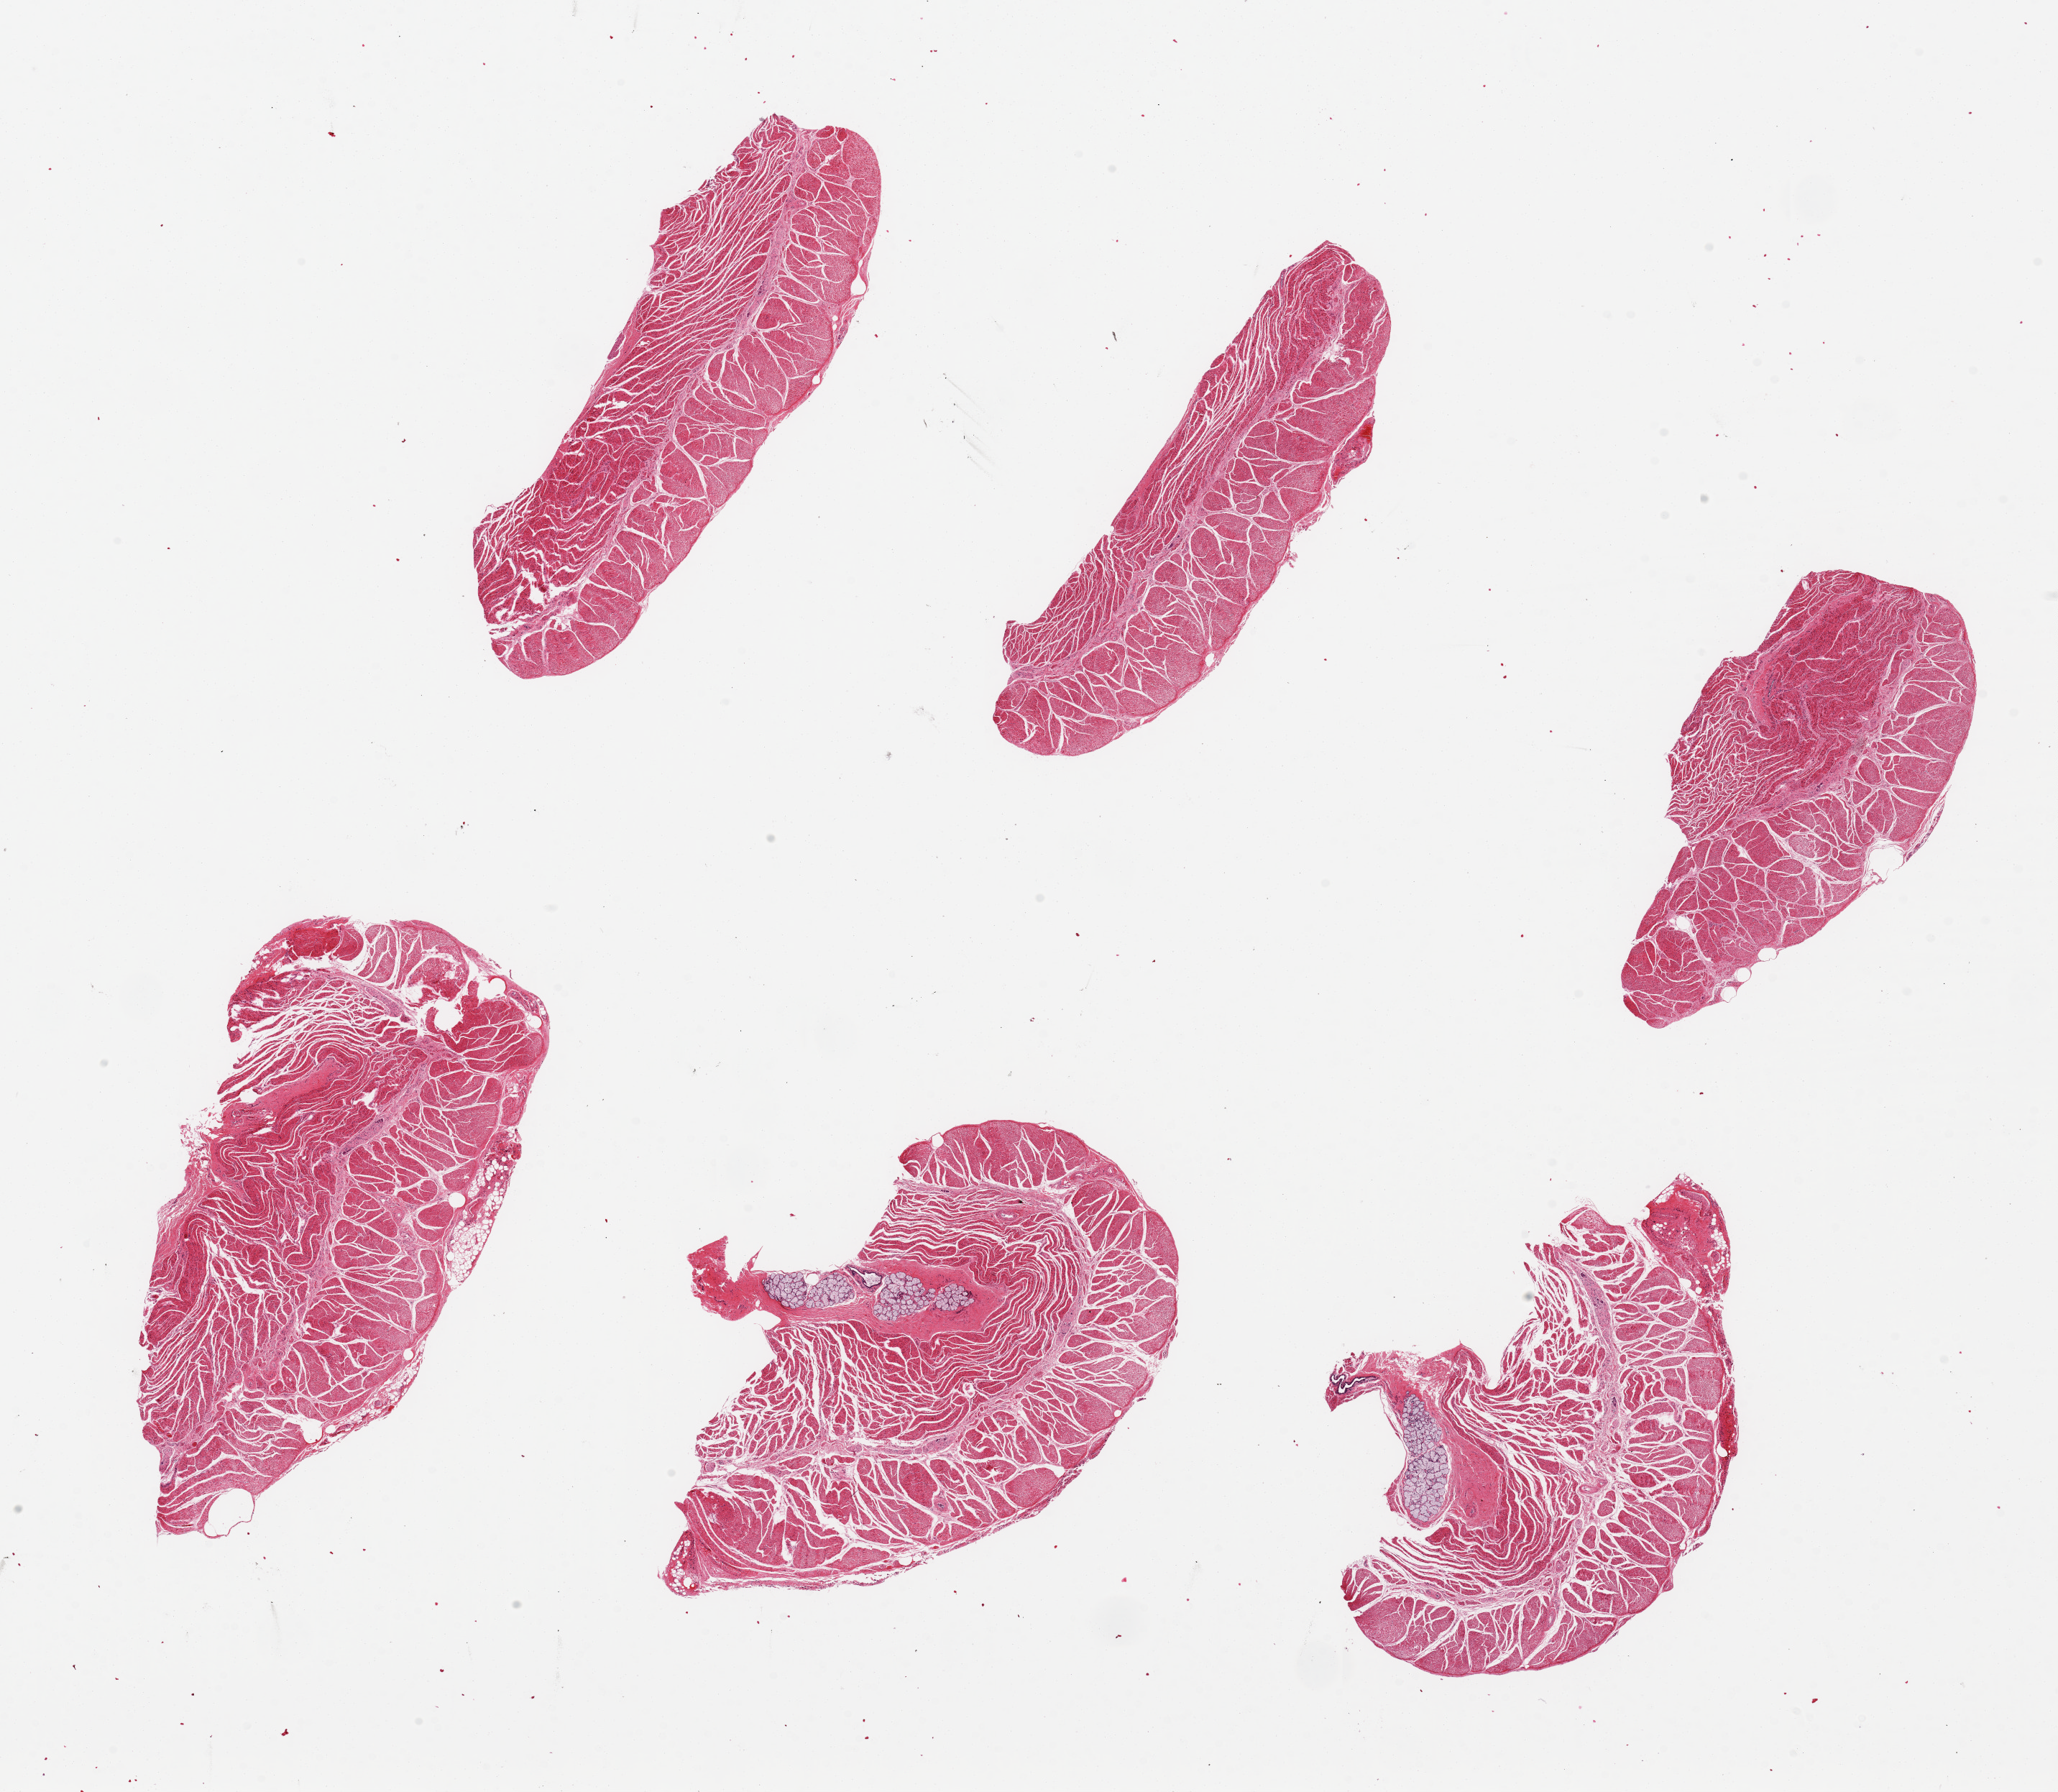
Whole-slide image, H&E stain, shown as a low-resolution overview of the whole scanned area (about 22.6 x 19.7 mm). PAXgene-fixed, paraffin-embedded tissue. Section of esophageal muscle (target tissue). Donor tissue sample. Donor: male.
Reviewer comment on this tissue sample: 6 pieces up to 7x3 mm; 2 have submucosal glands <10% of each aliquot.